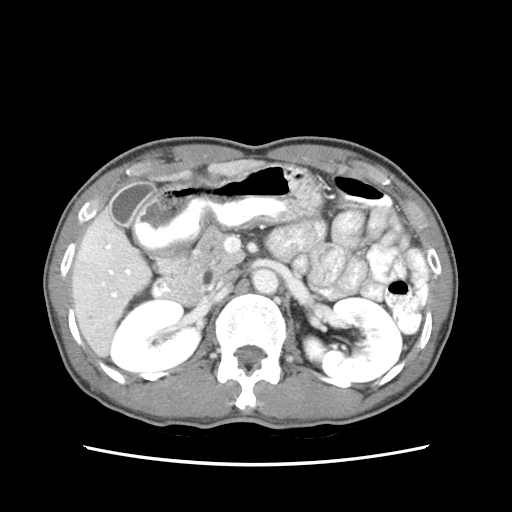
Contrast-enhanced abdominal CT (liver protocol), one axial slice; position 28 of 79 along the scan axis; reconstruction kernel STANDARD; 120 kVp; soft-tissue window (W 400 / L 40 HU); 2.5 mm slice thickness; 512 × 512 image matrix, field of view 320 × 320 mm. From the clinical record (not read from this slice): diagnosis: hepatocellular carcinoma (patient treated with transarterial chemoembolisation; whether this scan precedes or follows treatment is not stated here); TNM stage (as recorded): Stage-IIIB; Child-Pugh class: A; tumour differentiation: moderately differentiated; tumour nodularity: multinodular.
Structures marked on this image (semi-automatically segmented with operator editing):
- liver parenchyma outside the tumour (the mass and vessels are separate outlines, so this box may not span the whole liver): bounding box (x1, y1, x2, y2) in pixels: (72, 160, 252, 356)
- liver vessels: (89, 223, 142, 327)